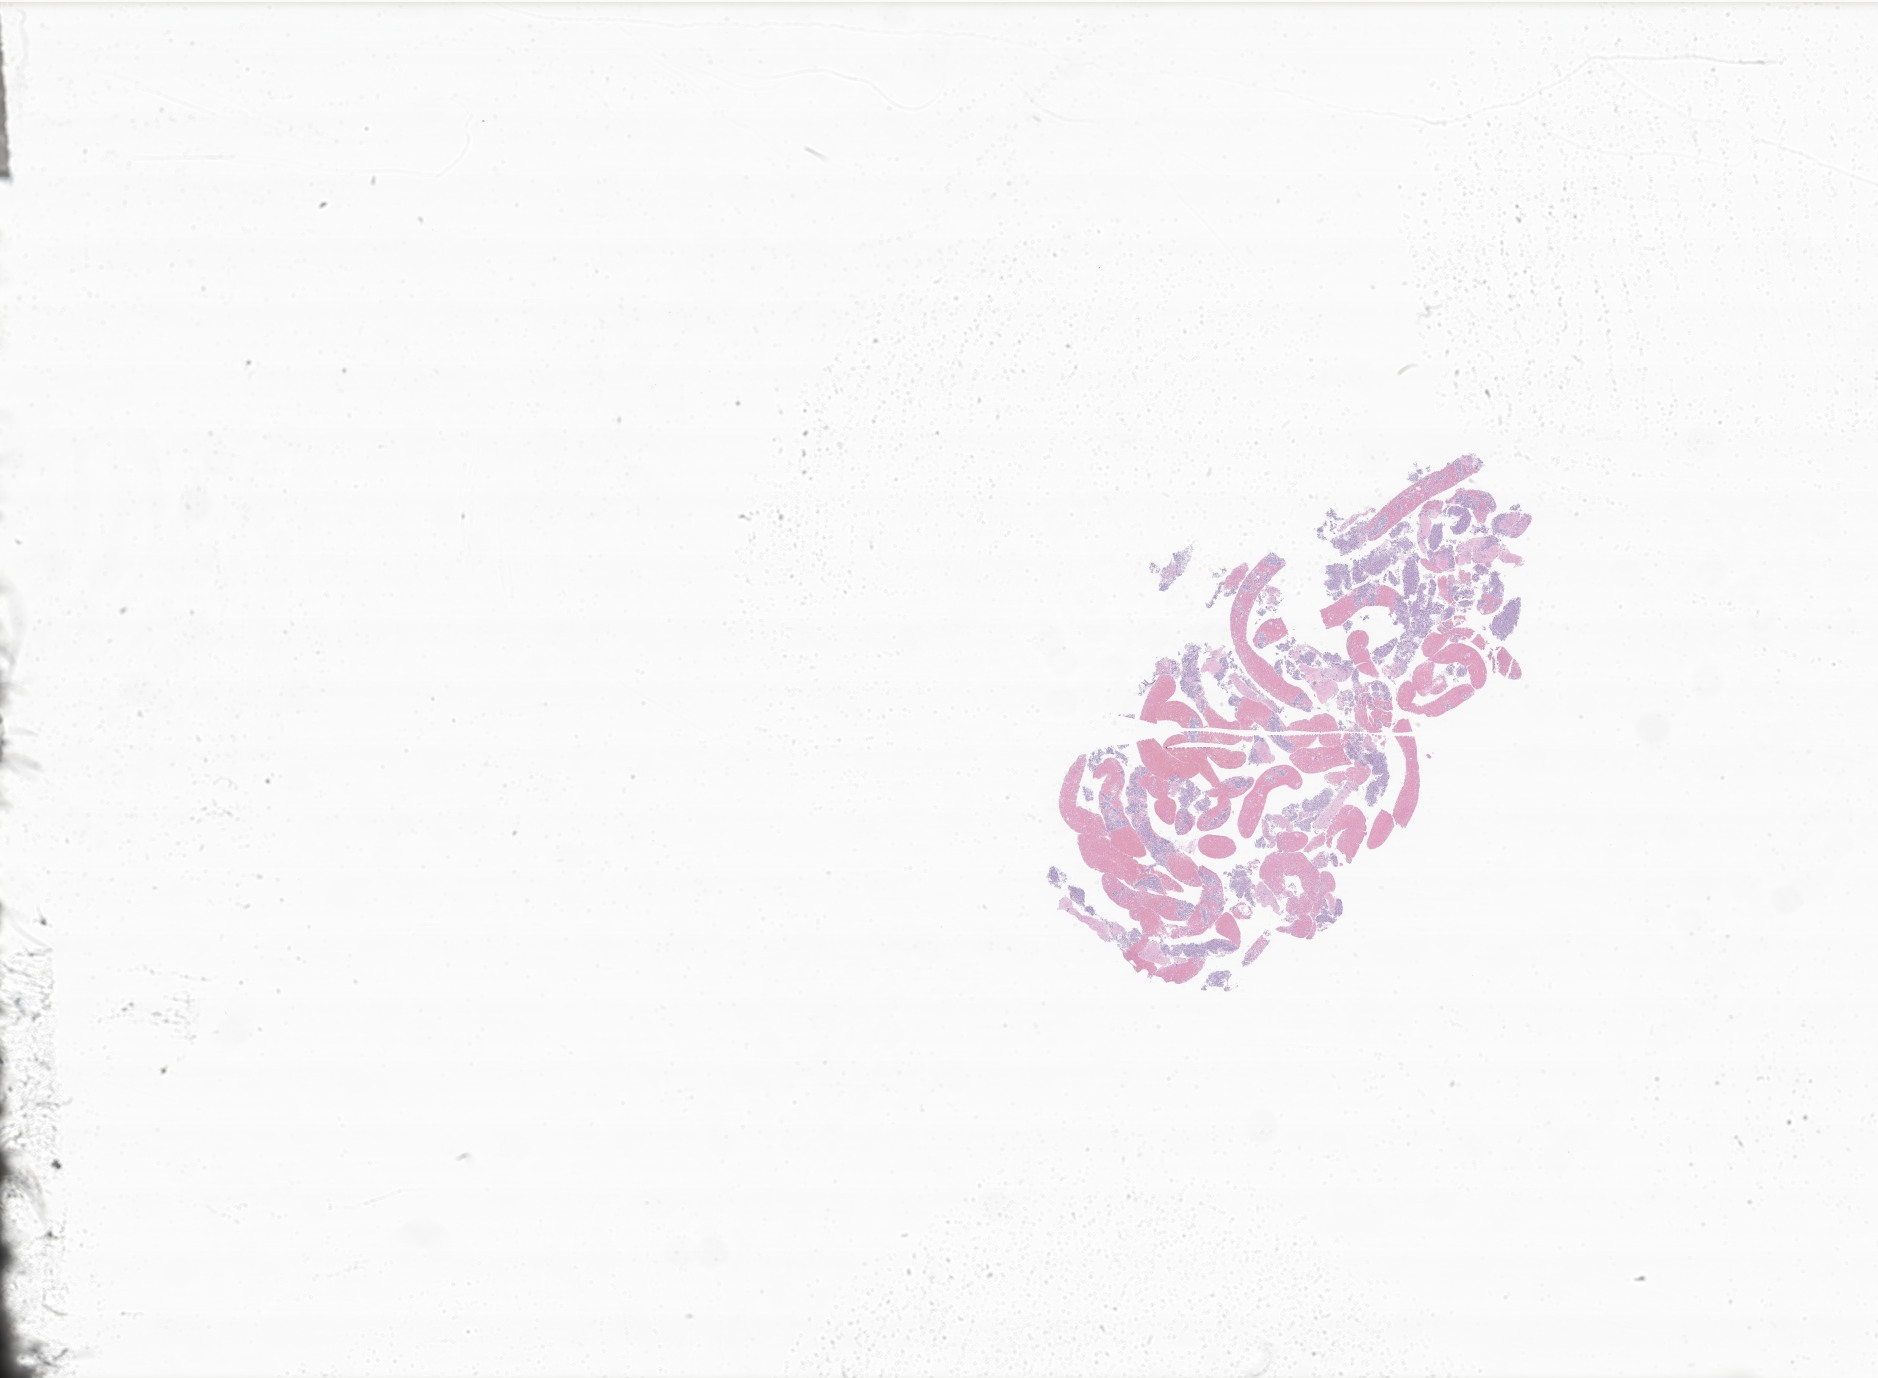
Whole-slide image, haematoxylin and eosin stain of tumor tissue from the pyloric antrum — shown as a low-resolution overview of the whole scanned area (about 31.7 x 23.2 mm), FFPE section. Patient male; age 216 months (18 years).
• recorded diagnosis: Gastrointestinal stromal tumor
• tissue or organ of origin (case record): gastric antrum